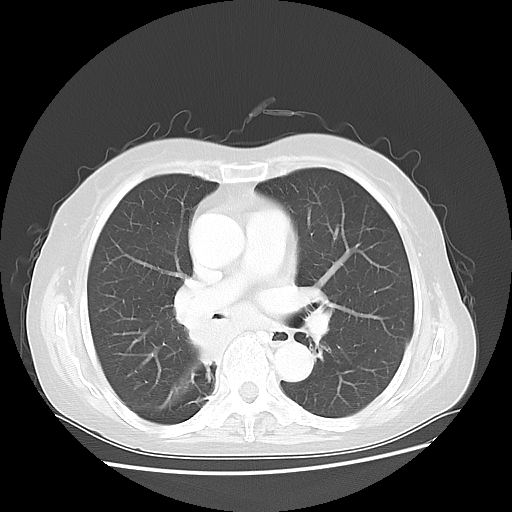
Chest CT, one axial slice. Position 26 of 47 along the scan axis. Reconstruction kernel LUNG. Lung window (W 1500 / L -600 HU). 5 mm slice thickness. 512 × 512 image matrix. Patient: female, 63 years. From the clinical record (not read from this slice): clinical TNM (as recorded): T2 N3 M1b; histopathological grade: G3.
Outlined on this slice (rectangle marked by the reading radiologist):
- lung tumour (recorded histology: small cell carcinoma): bounding box <183,314,228,374> (left, top, right, bottom; pixels)